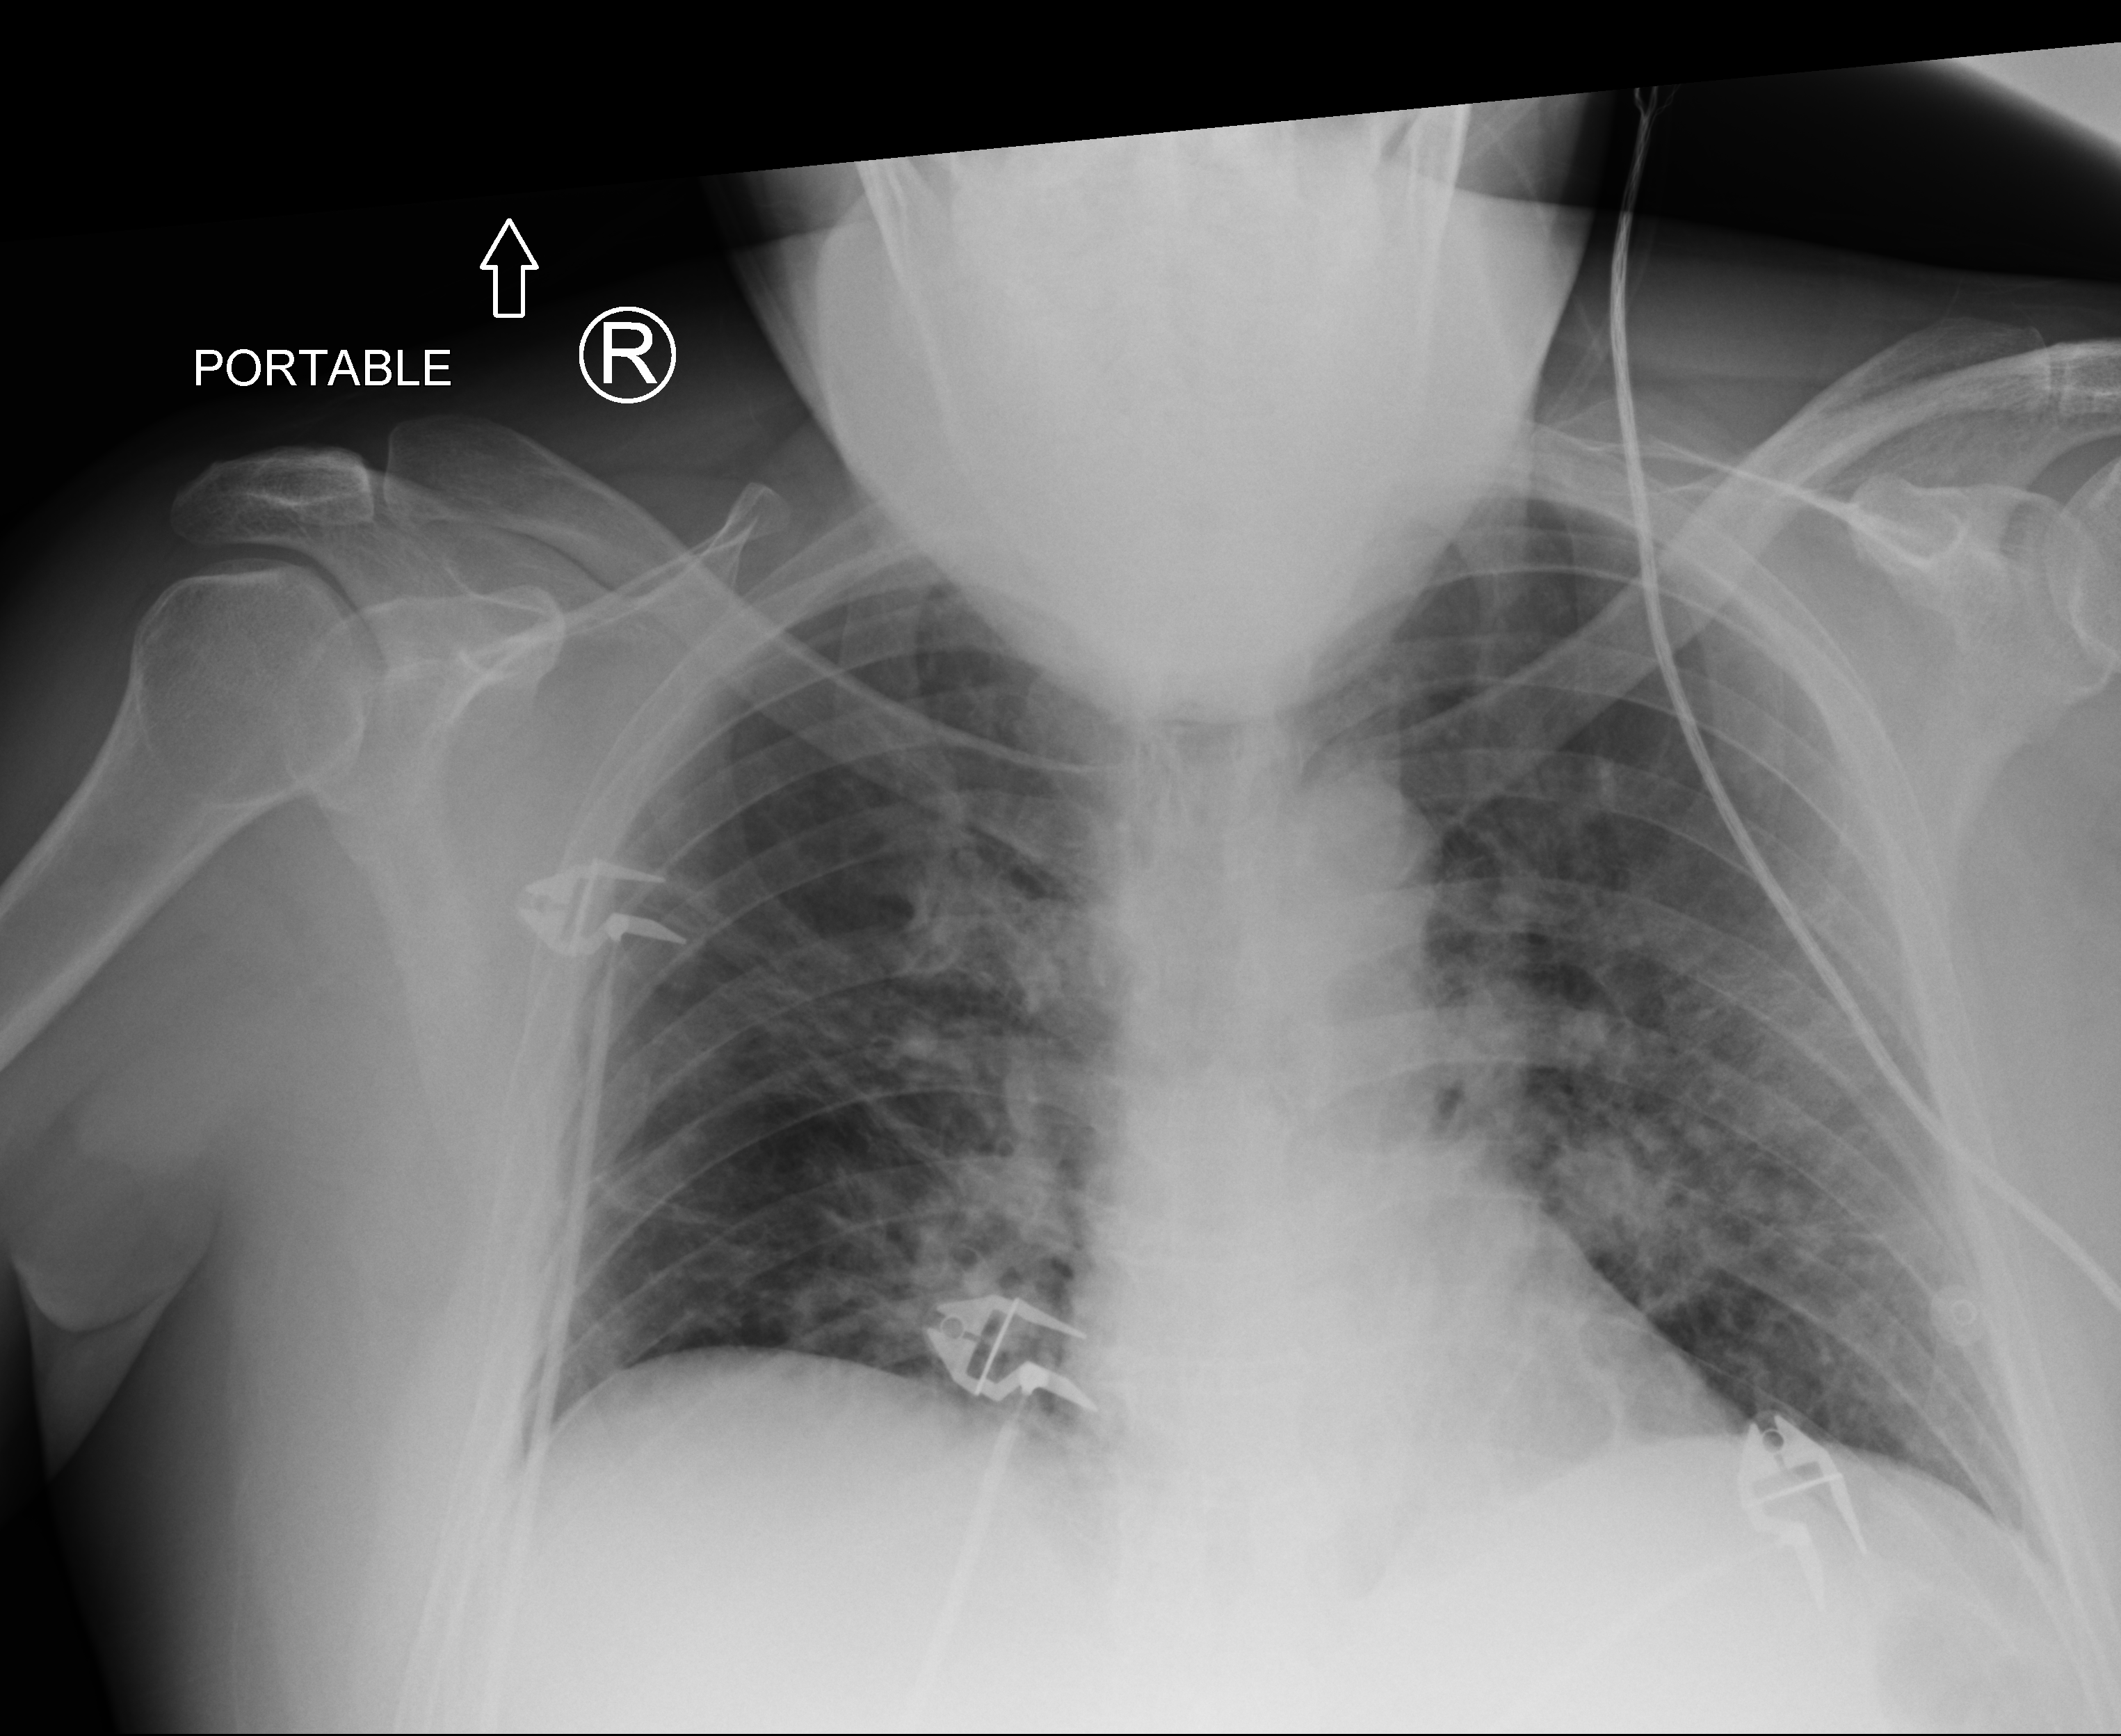
Chest X-ray (portable); anteroposterior (AP) projection. Male patient hospitalised with COVID-19, age 18–59 years.
Hospital-stay facts (about this admission, not read from this image; timing relative to this image not recorded): diabetes (admission record): no.